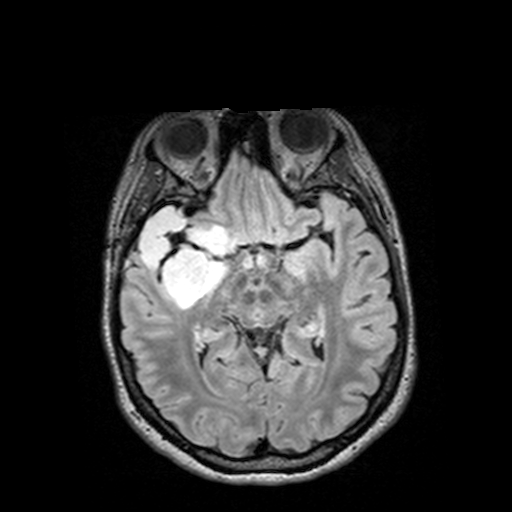
Brain MRI from a brain-tumour surgery series, one axial slice; slice 81 of 144 in the series (ordered by position); T2 FLAIR; 512 × 512 image matrix, field of view 250 × 250 mm. Case-level facts recorded for this patient, not image findings: histopathology: Astrocytoma; WHO grade: 3; IDH mutation: yes; tumour location: Right Insular Temporal.
Annotated regions visible in this slice (expert manual segmentation):
- tumour: bounding box <126,209,232,307> (left, top, right, bottom; pixels)